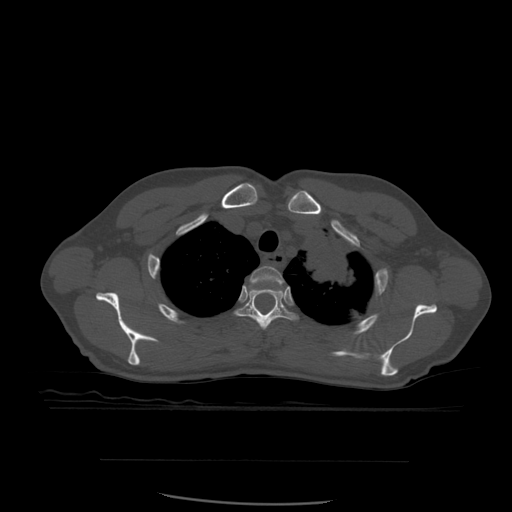
CT including the spine, one axial slice. Position 445 of 574 along the scan axis. Bone window (W 1800 / L 400 HU). 1.25 mm slice thickness. 512 × 512 image matrix, field of view 392 × 392 mm. Patient age 48 years. Case-level facts recorded for this patient, not image findings: primary cancer: lung; vertebrae with lytic lesions (as recorded): T11.
Annotated regions visible in this slice (semi-automatic segmentation, software-assisted and operator-edited):
- T2 vertebra: bounding box [x1, y1, x2, y2] px = [250, 266, 284, 294]
- T3 vertebra: [235, 285, 298, 331]